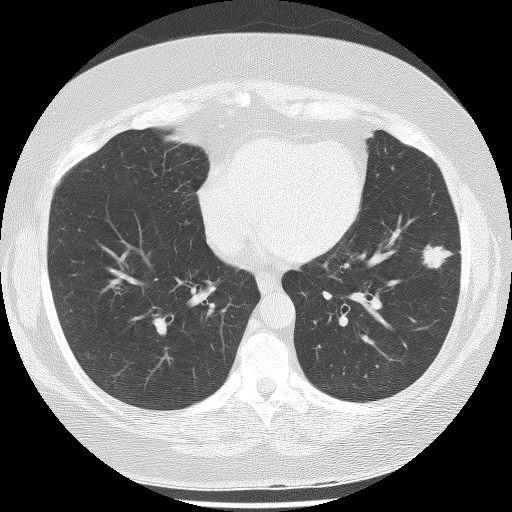
Low-dose screening chest CT, one axial slice. Slice 102 of 233 in the series (ordered by position). Reconstruction kernel BONE. Lung window (W 1500 / L -600 HU). 2.5 mm slice thickness. 512 × 512 image matrix, field of view 340 × 340 mm.
Structures marked on this image (outlined manually by an expert reader):
- lesion 1 (tumor, lower lobe of left lung): bounding box <422,244,452,269> (left, top, right, bottom; pixels)